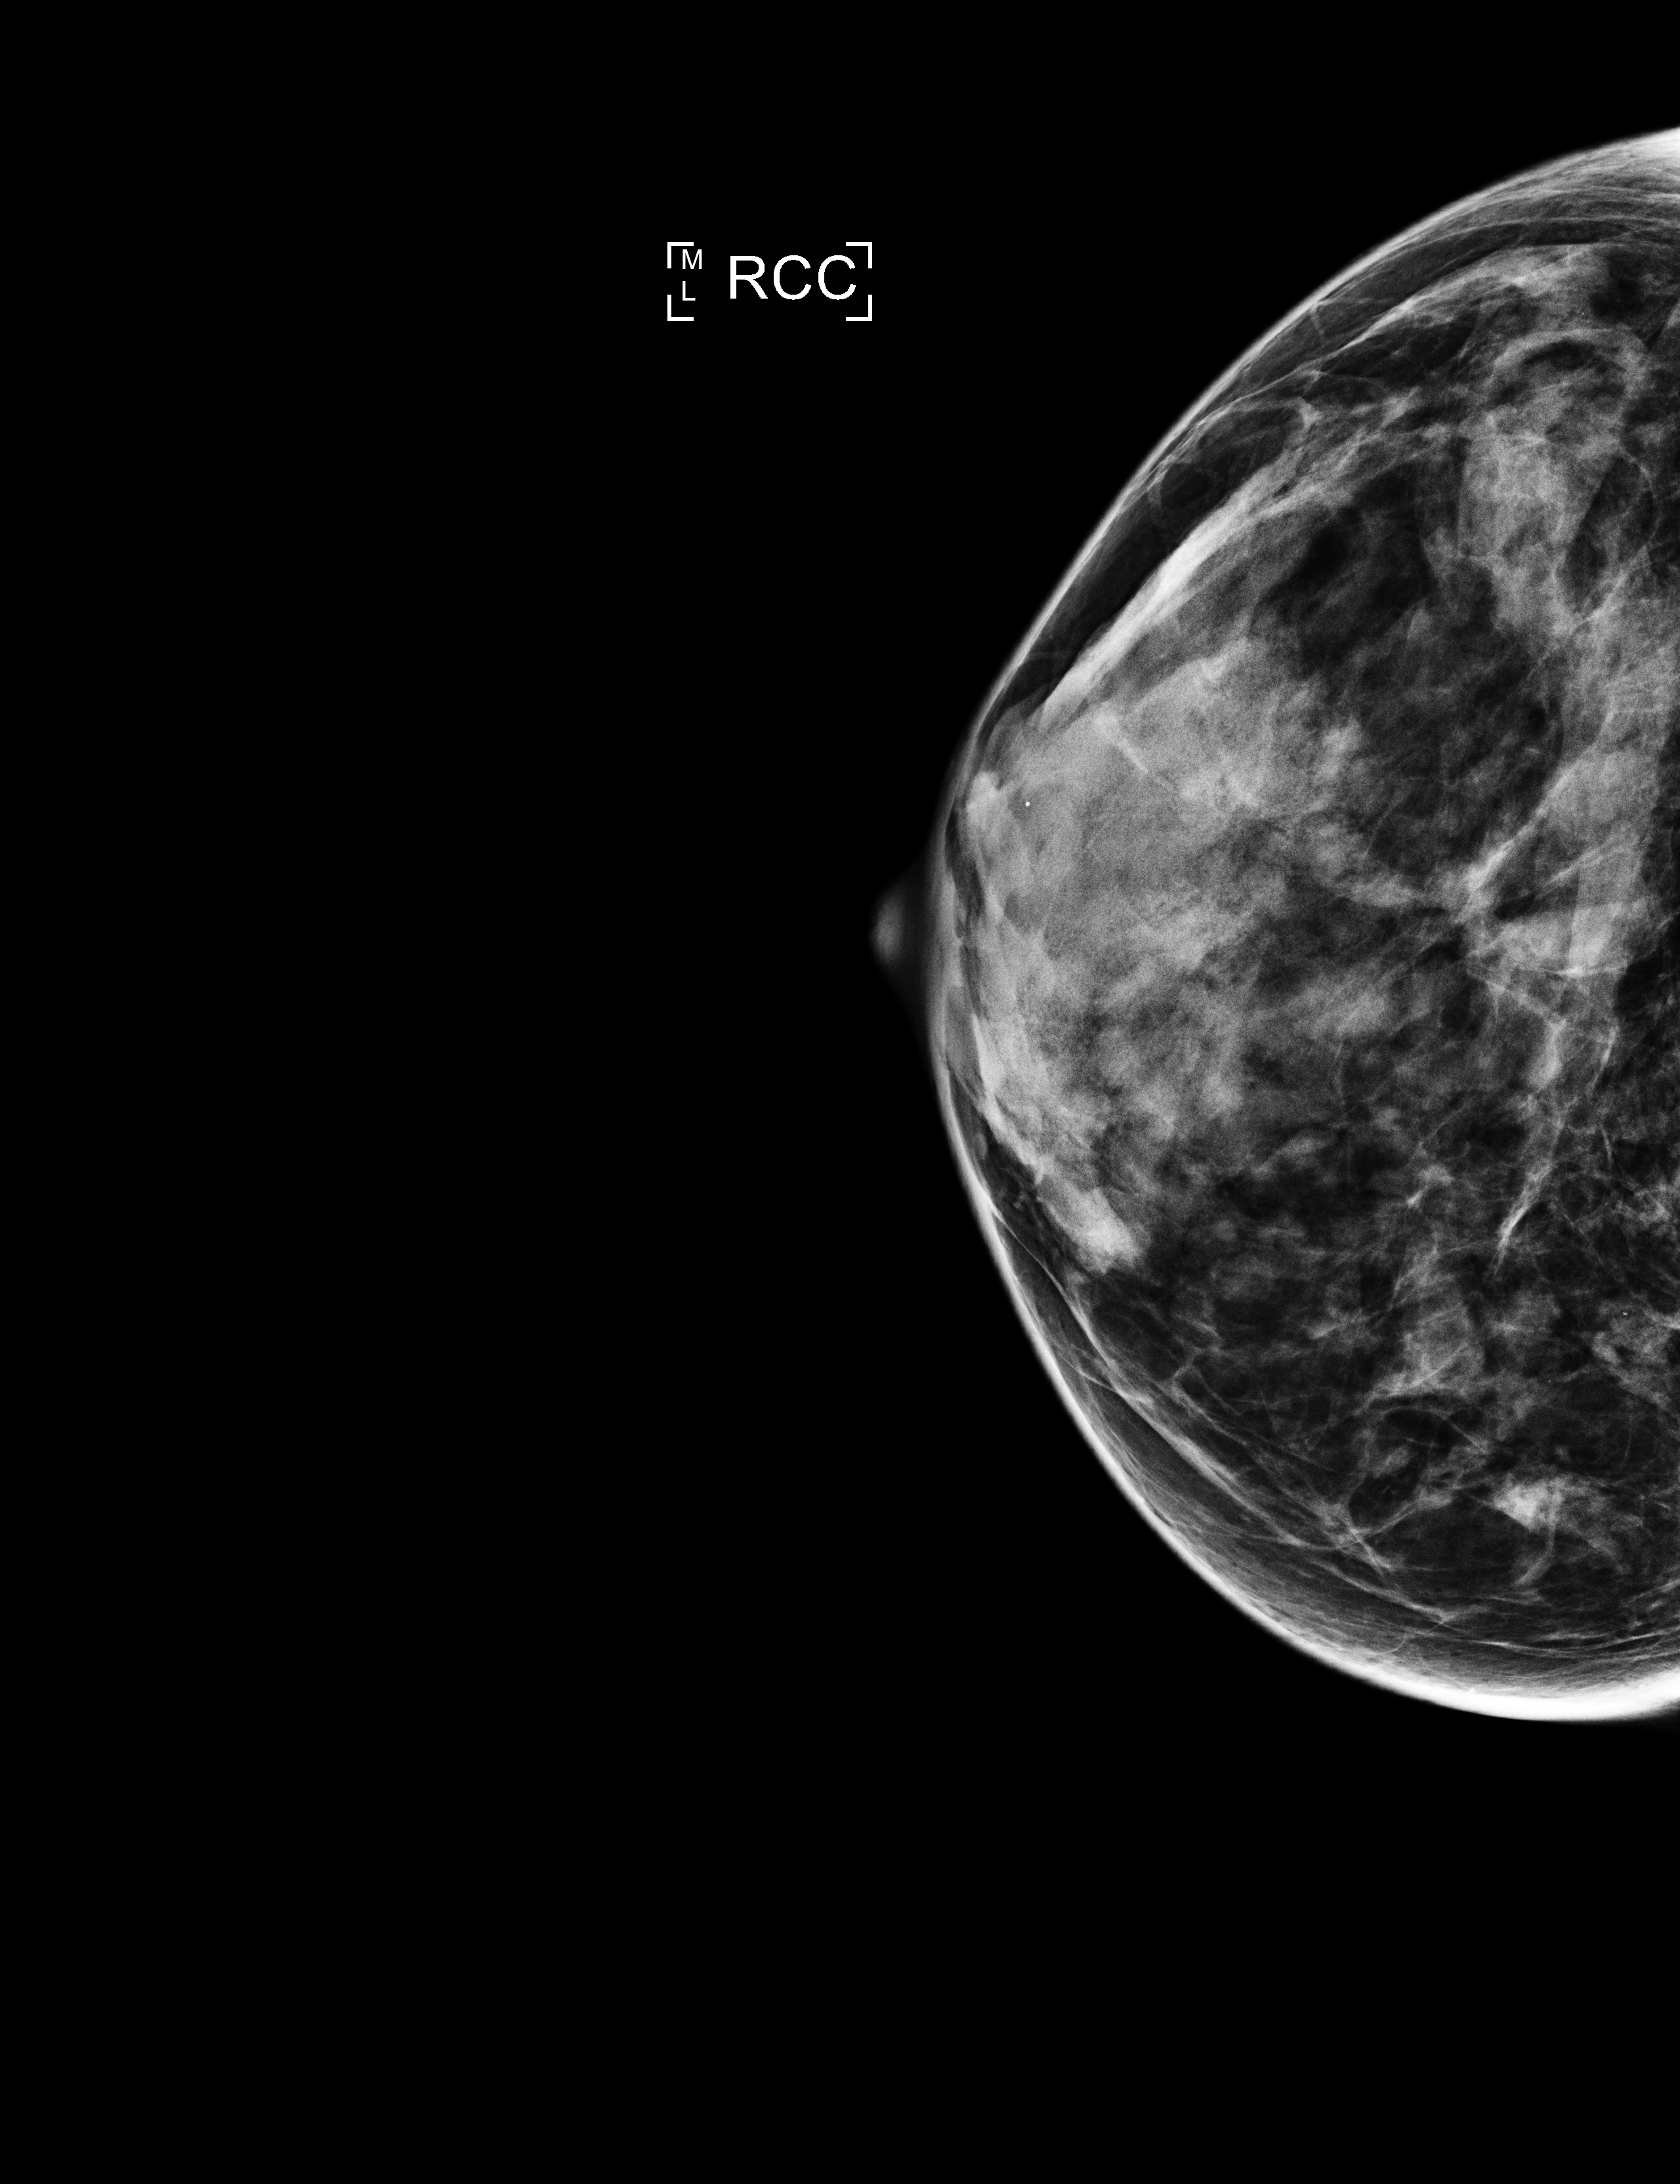
Full-field digital mammogram (FFDM), right breast, CC view, annual screening mammography examination, compressed breast thickness 40 mm, system: Selenia Dimensions. Patient: female, 52 years.
BI-RADS breast density category at the screening exam (both breasts, scale 1–4): 3. Final BI-RADS assessment for this screening round (tomosynthesis exam, both breasts): category 2. Recall: no recall after this screen.